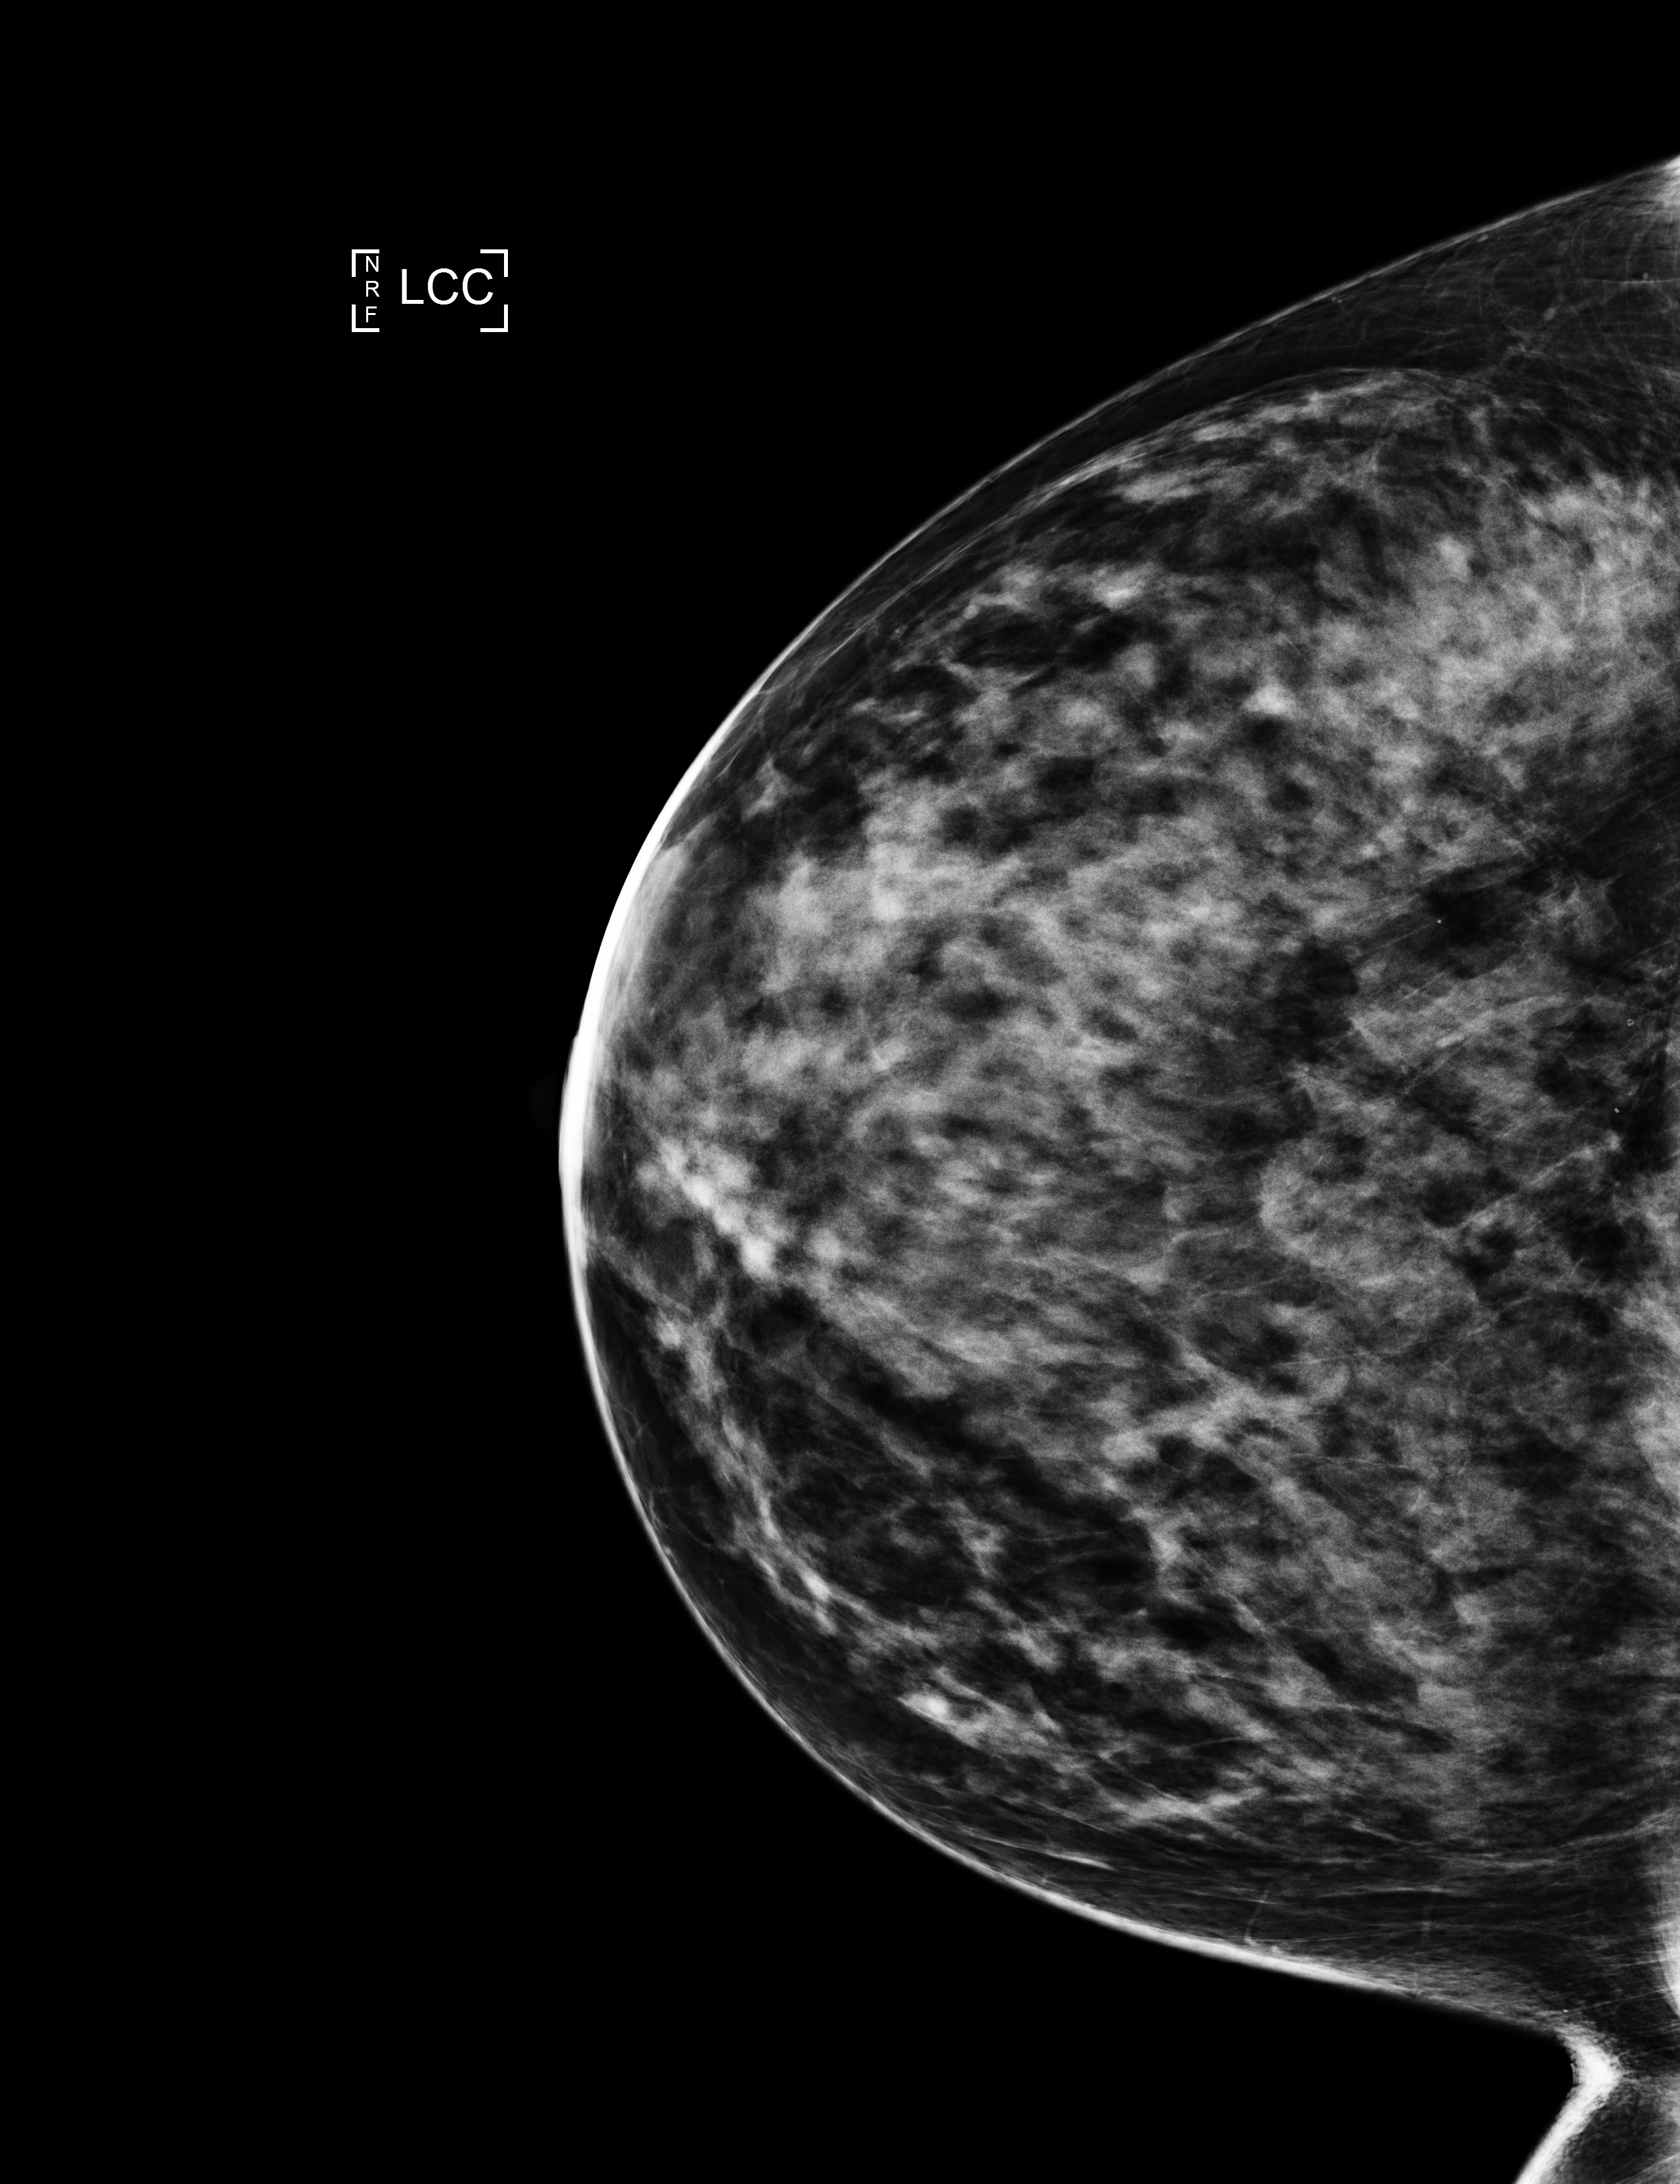
Digital mammogram (FFDM), left breast, craniocaudal (CC) view, screening examination, system: Selenia Dimensions. Patient aged 60 years (female).
BI-RADS breast density category at the screening exam (both breasts, scale 1–4): 4. Final BI-RADS assessment for this screening round (tomosynthesis exam, both breasts): category 1. Recall: no recall after this screen.